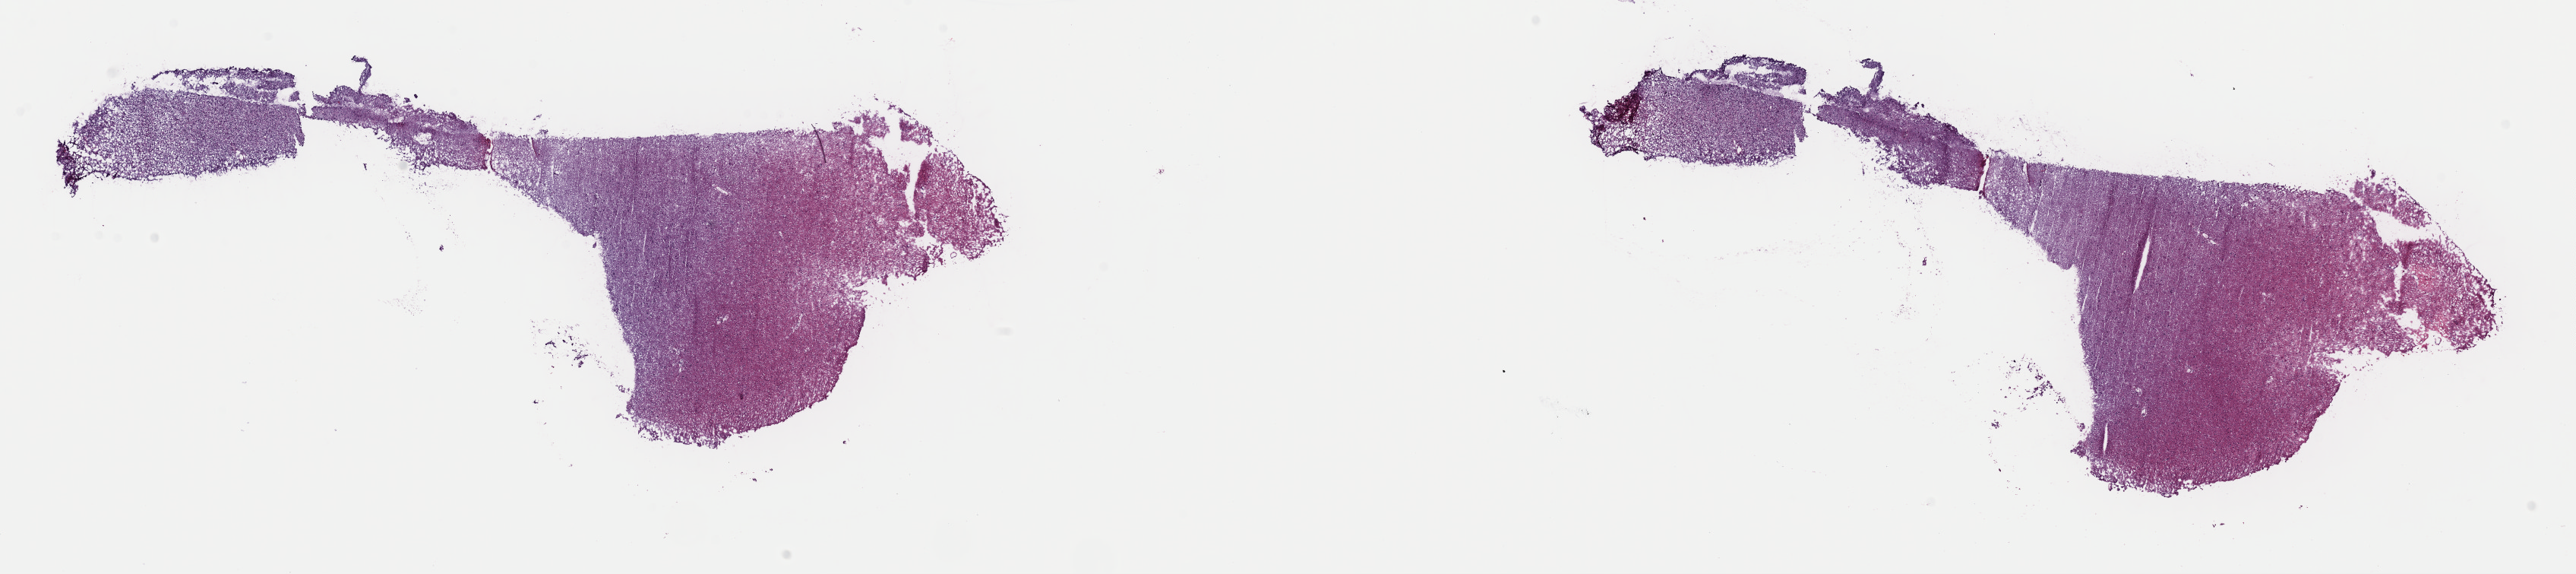
Digitized Hematoxylin and eosin (H&E) stained tissue section (whole slide) — a low-resolution overview of the entire scanned area, about 26.8 x 6.0 mm (from a 40x scan); frozen section from the top of the tissue portion; primary tumour sample from the brain. Female patient; age at initial diagnosis 53 years. Histologic grade: G3 (poorly differentiated). Slide review estimates, as recorded: tumour cells 80%, tumour nuclei 90%, normal cells 10%, stromal cells 10%, necrosis 0%. Inflammatory infiltration, as recorded: lymphocyte infiltration 0%, monocyte infiltration 0%, neutrophil infiltration 0%.
• diagnosis: Mixed glioma
• laterality: left